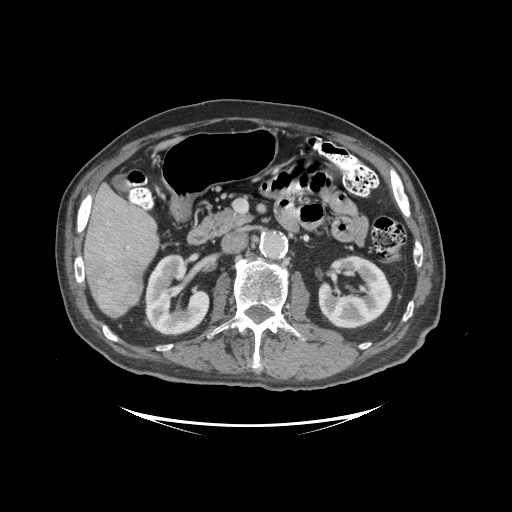
Contrast-enhanced abdominal CT (liver protocol), one axial slice. Slice 43 of 99 in the series (ordered by position). 140 kVp. Soft-tissue window (W 400 / L 40 HU). 512 × 512 image matrix, field of view 460 × 460 mm. From the clinical record (not read from this slice): diagnosis: hepatocellular carcinoma (patient treated with transarterial chemoembolisation; whether this scan precedes or follows treatment is not stated here); TNM stage (as recorded): Stage-I; Child-Pugh class: A; tumour differentiation: moderately differentiated.
Structures marked on this image (semi-automatic segmentation, software-assisted and operator-edited):
- liver parenchyma outside the tumour (the mass and vessels are separate outlines, so this box may not span the whole liver): bounding box [x1, y1, x2, y2] px = [84, 184, 158, 318]
- mass: [87, 257, 142, 314]